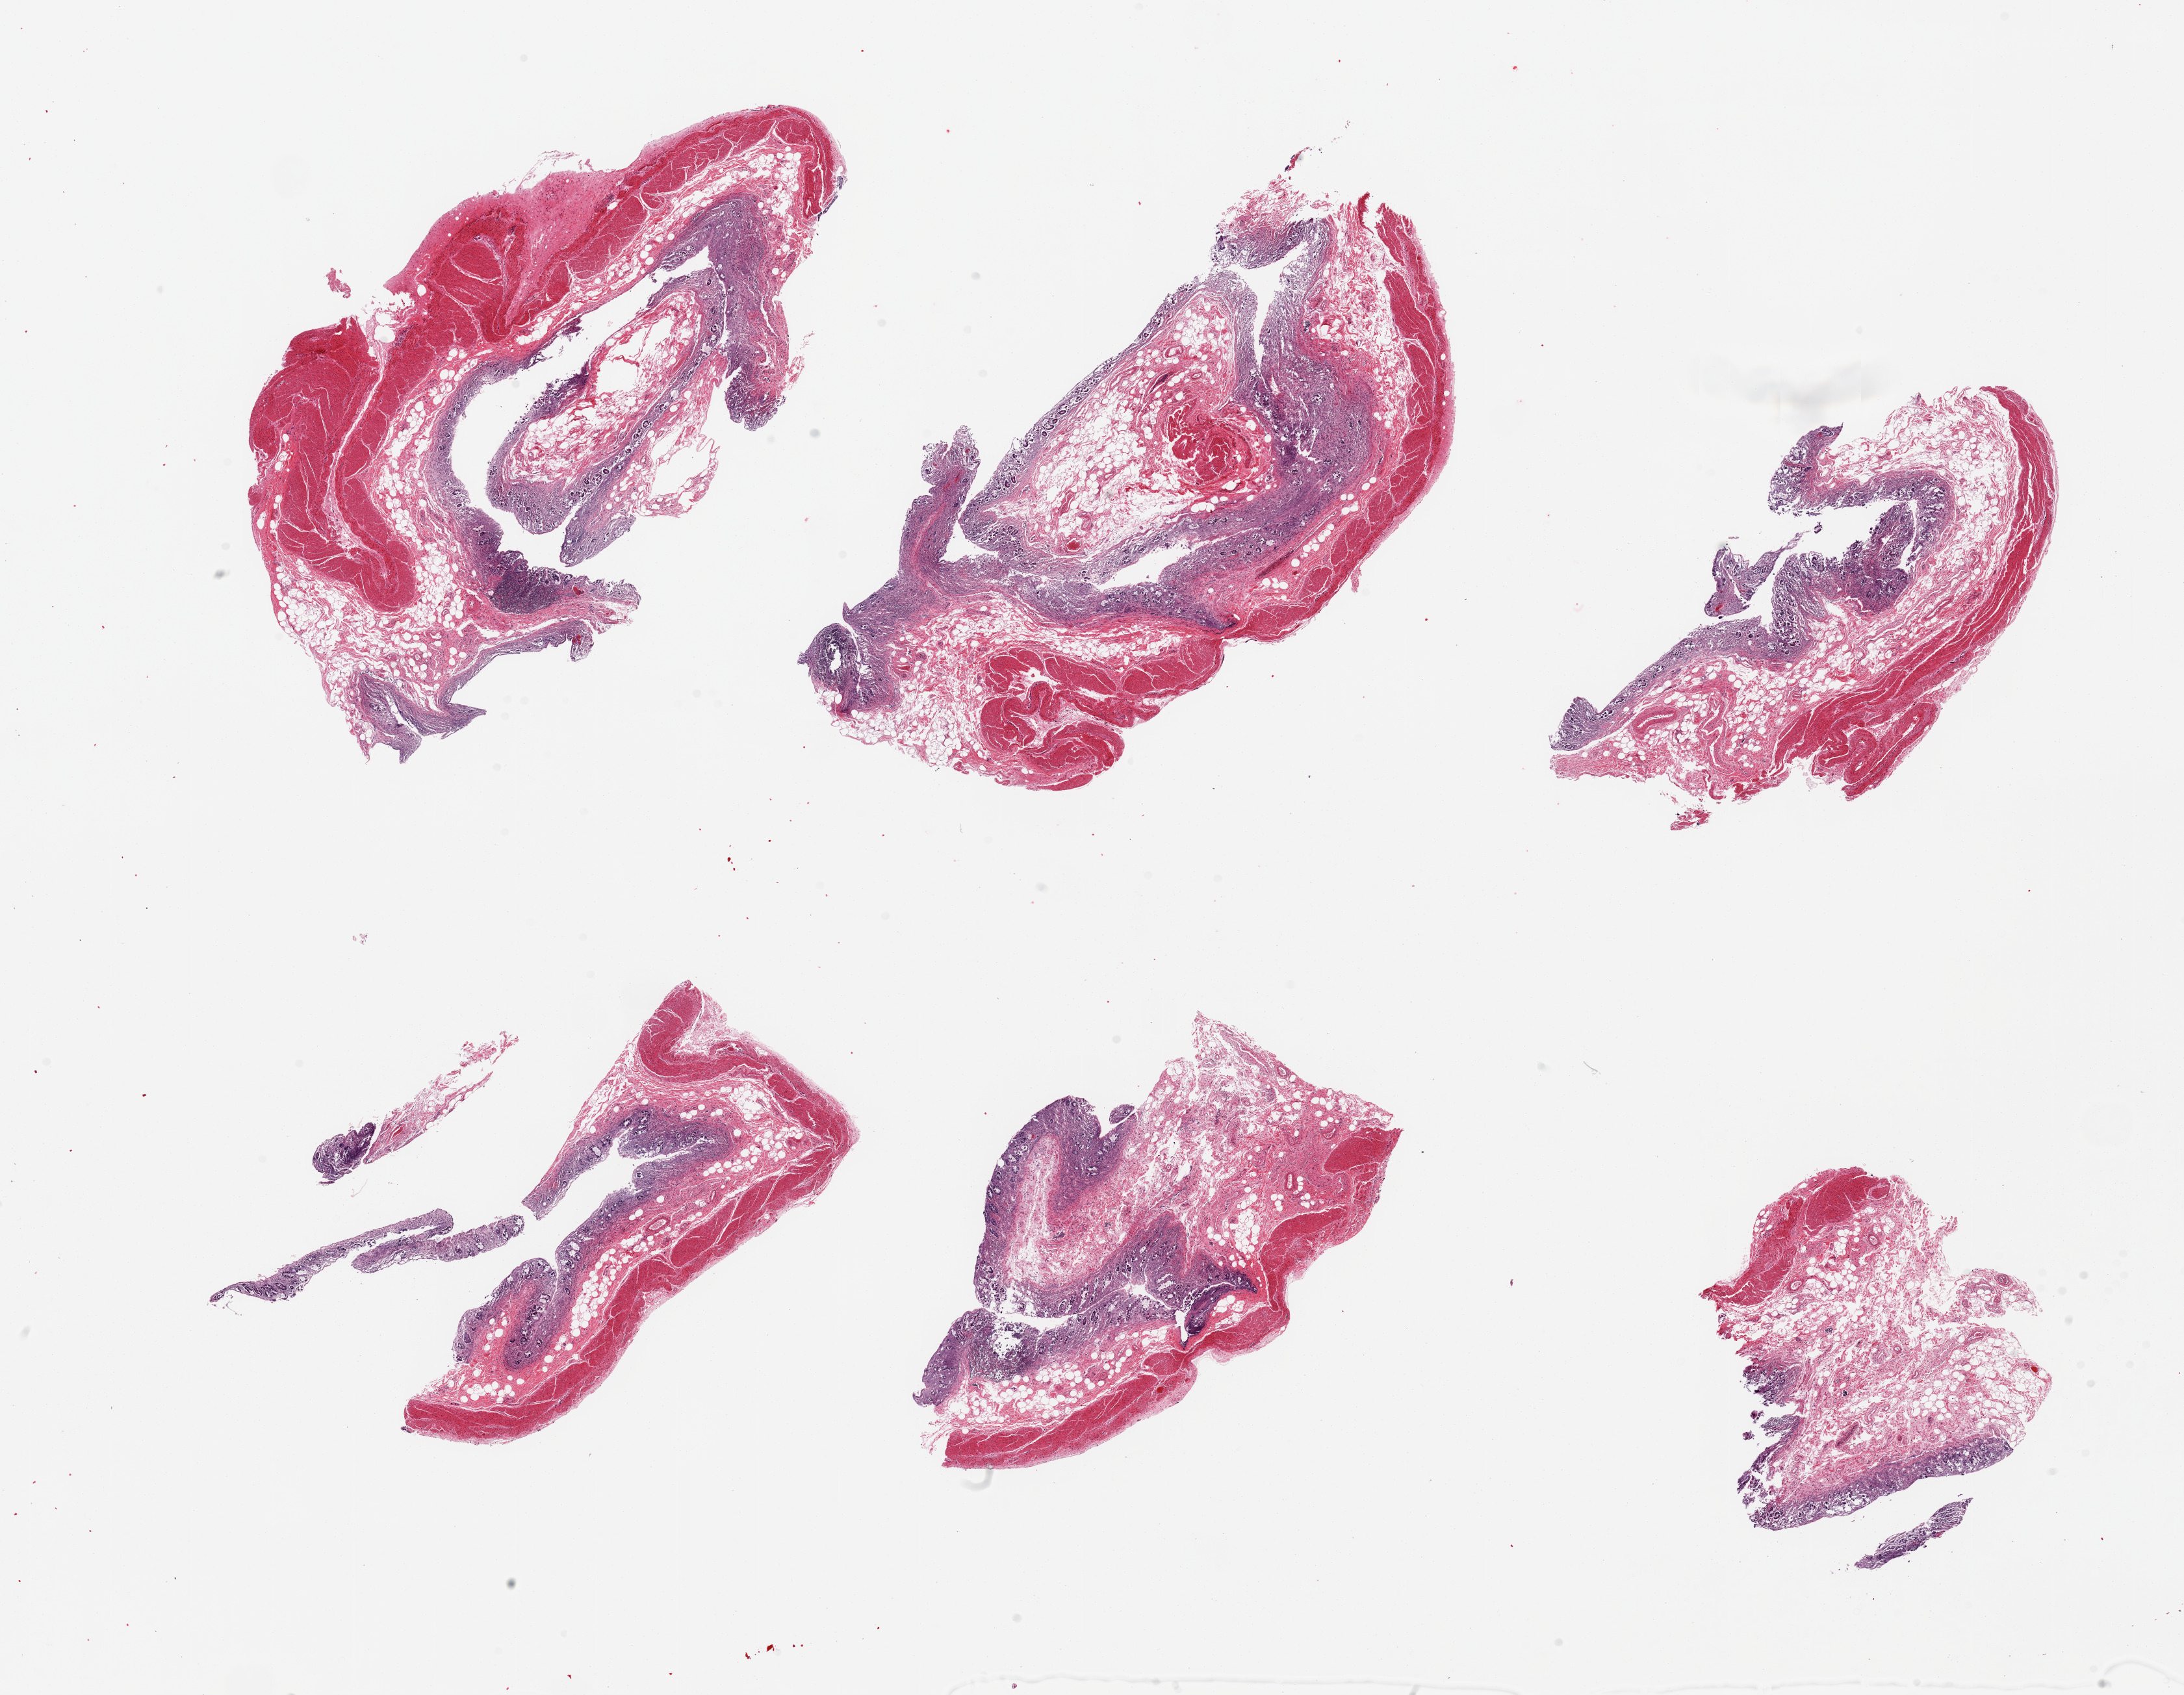
Whole-slide image, haematoxylin and eosin stain, low-resolution overview of the scanned area, about 26.6 x 20.6 mm; PAXgene-fixed paraffin-embedded (PFPE) section; section of transverse colon (target tissue); donor tissue sample. Male donor.
• reviewer comment on this tissue sample: 6 pieces; autolyzed mucosa, thick fatty submucosa, preserved thin muscularis